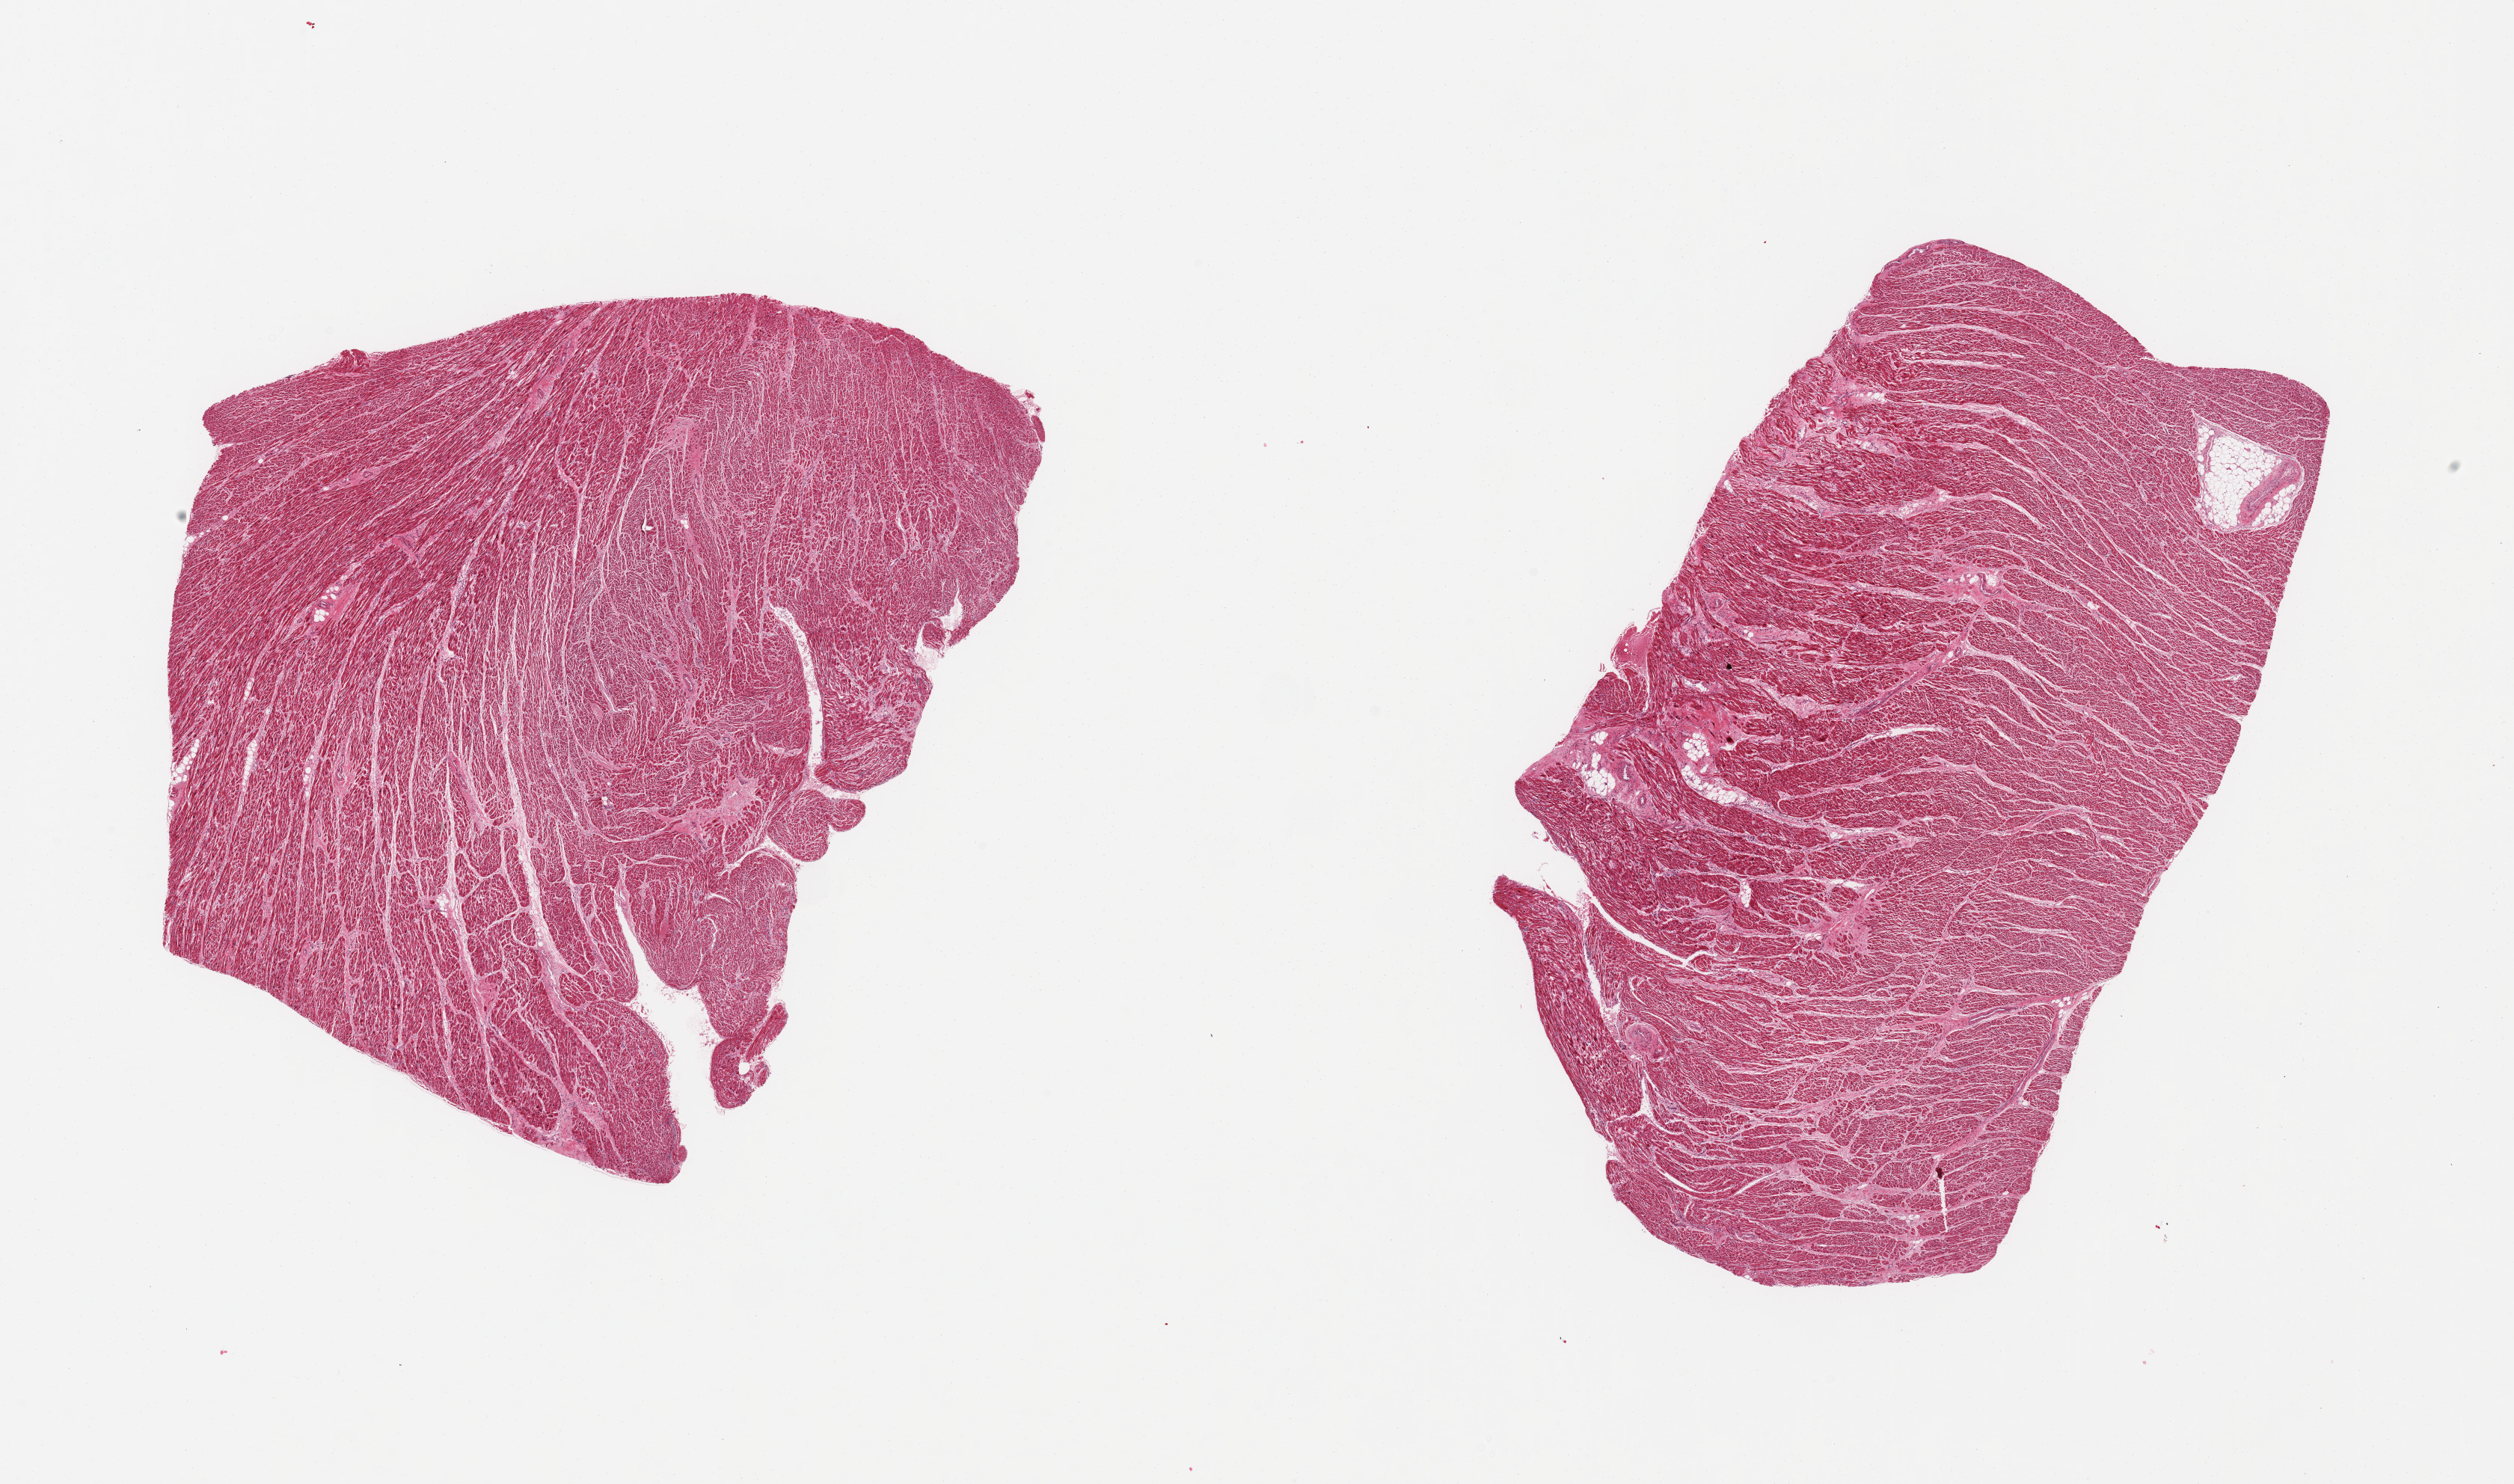
H&E whole-slide image, brightfield, whole scanned area (about 26.6 x 15.7 mm, from a 20x scan) shown as a low-resolution overview; PAXgene-fixed paraffin-embedded (PFPE) section; sampled site (target tissue): heart; tissue donor sample.
Pathologist's review note for this sample: 2 pieces evidence of acute infarction.